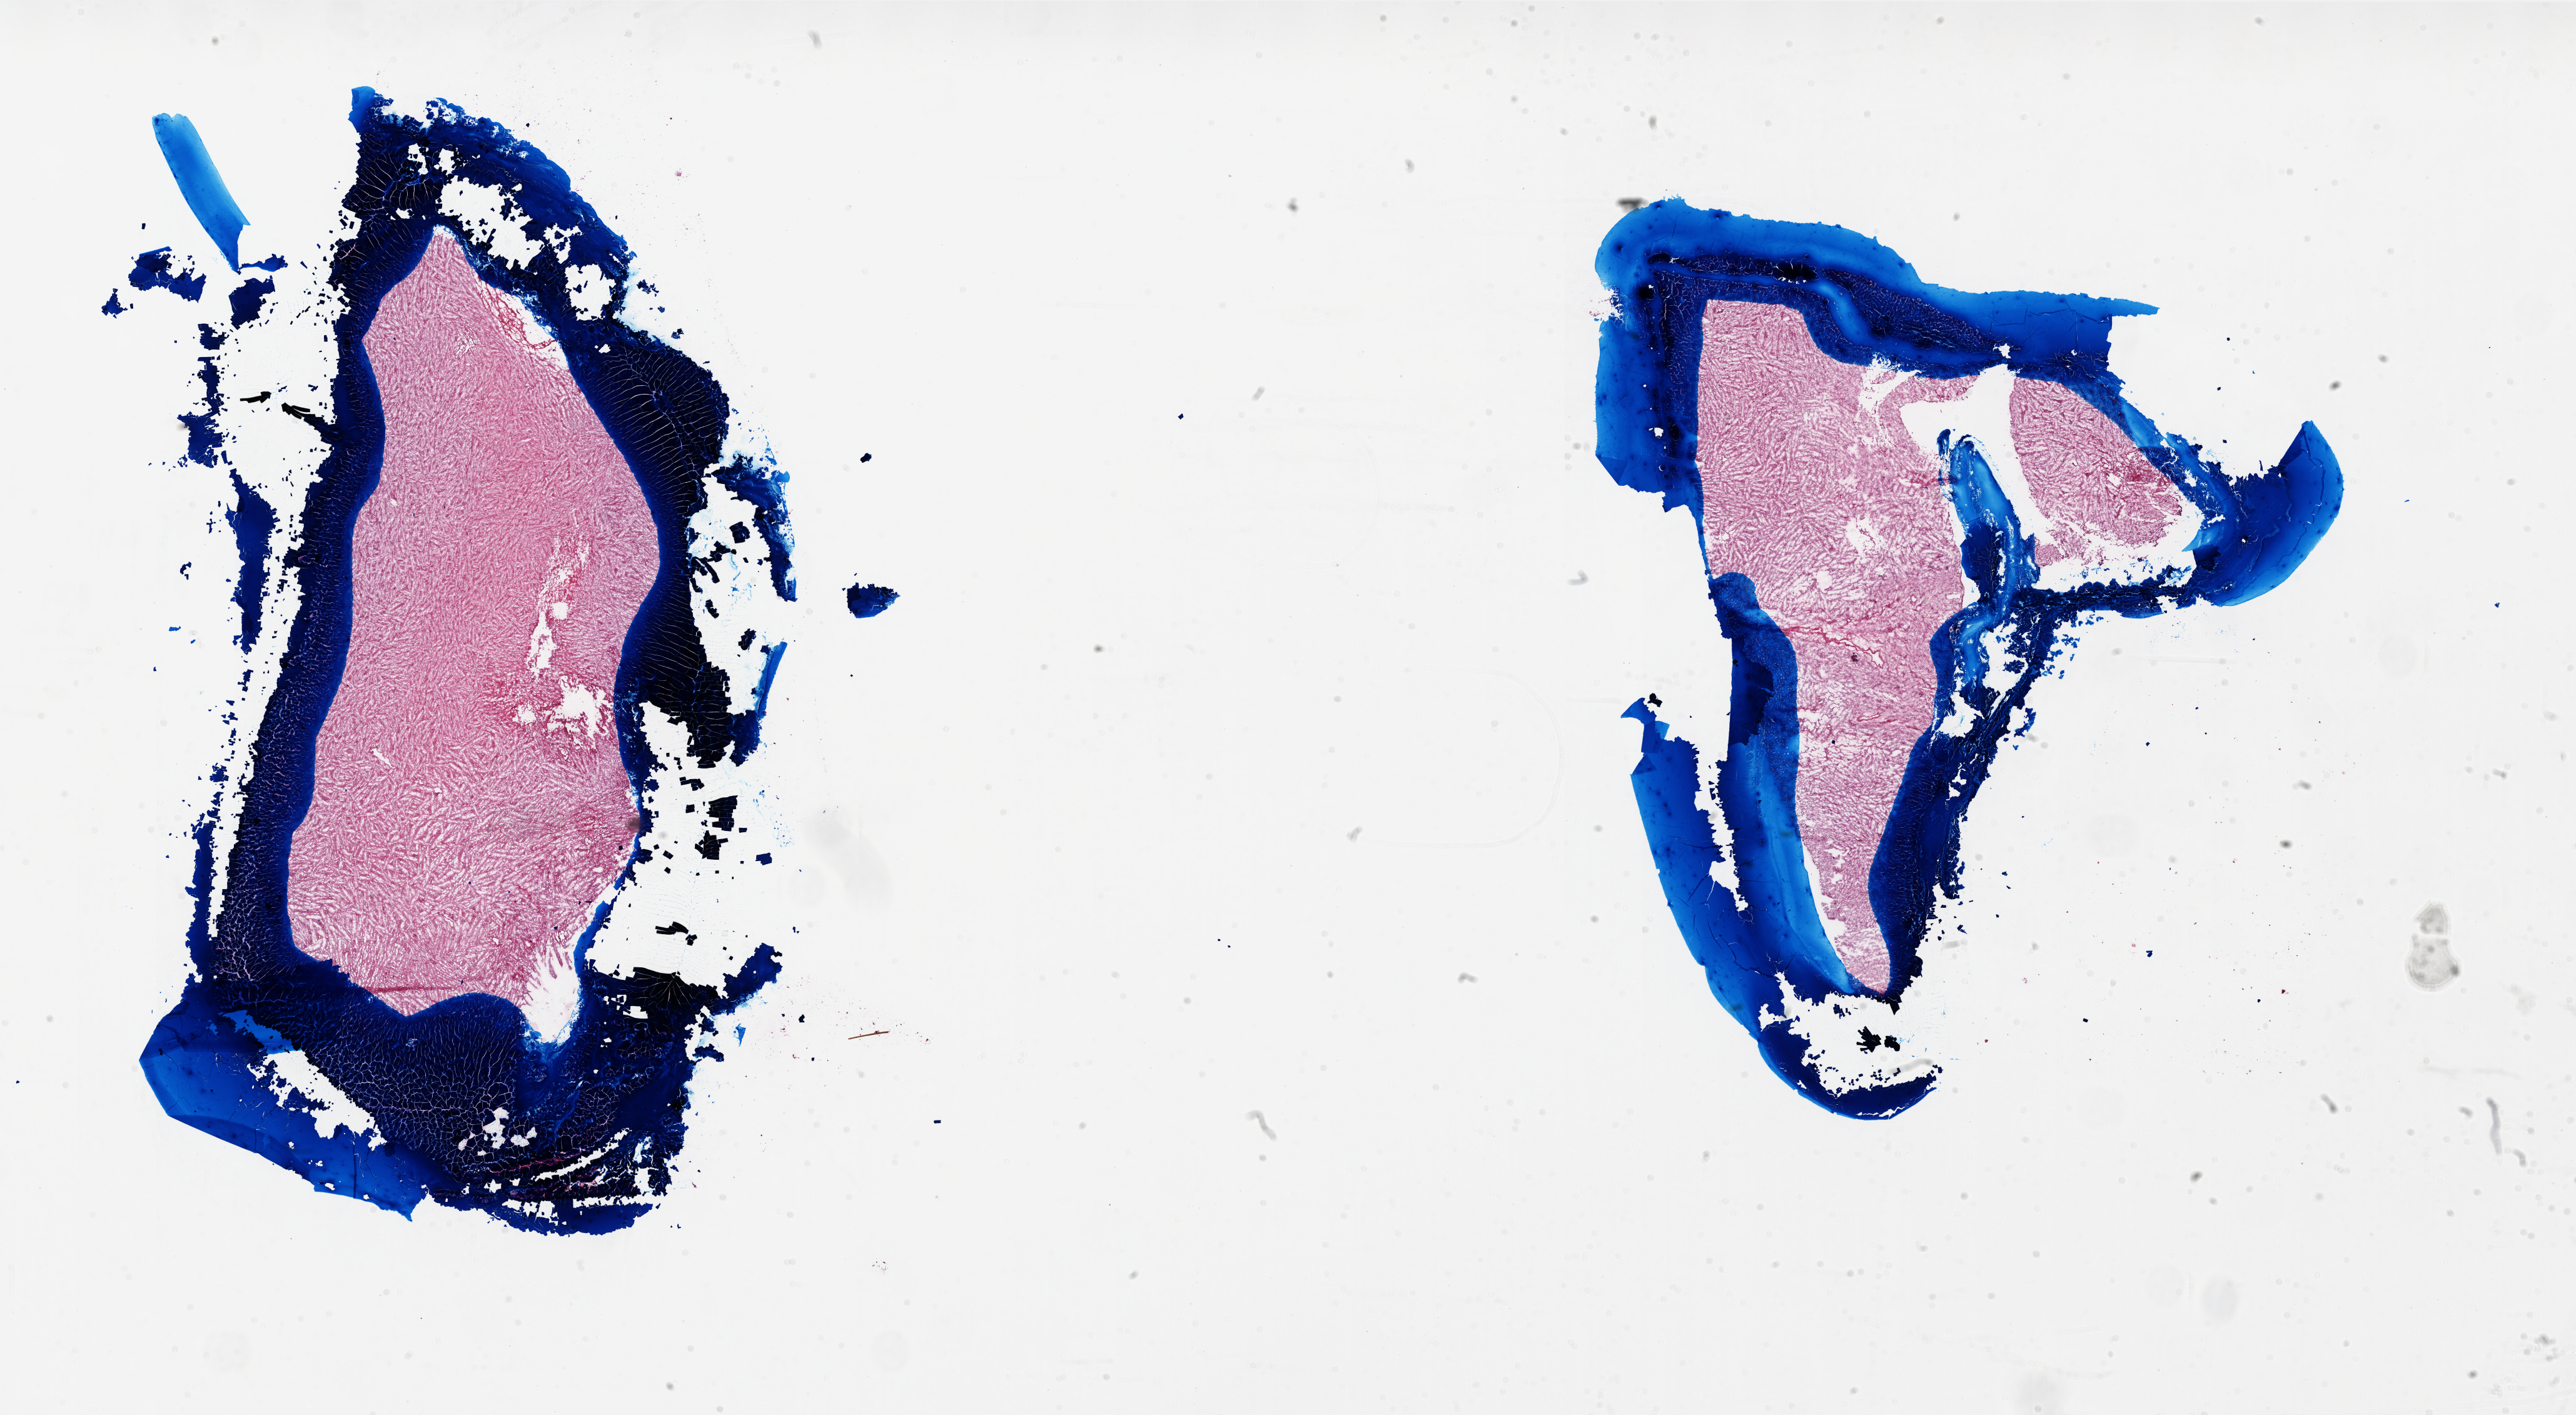
Digitized H&E tissue section (whole slide), shown as a low-resolution overview of the whole scanned area (about 33.0 x 18.1 mm, from a 20x scan); frozen section from the top of the tissue portion; primary tumour sample from the brain. Patient: male, age at initial diagnosis 52 years. Pathologist review of this section (percent, as recorded): tumour cells 100%, tumour nuclei 100%, normal cells 0%, stromal cells 0%, necrosis 0%.
Pathologic diagnosis: Glioblastoma.